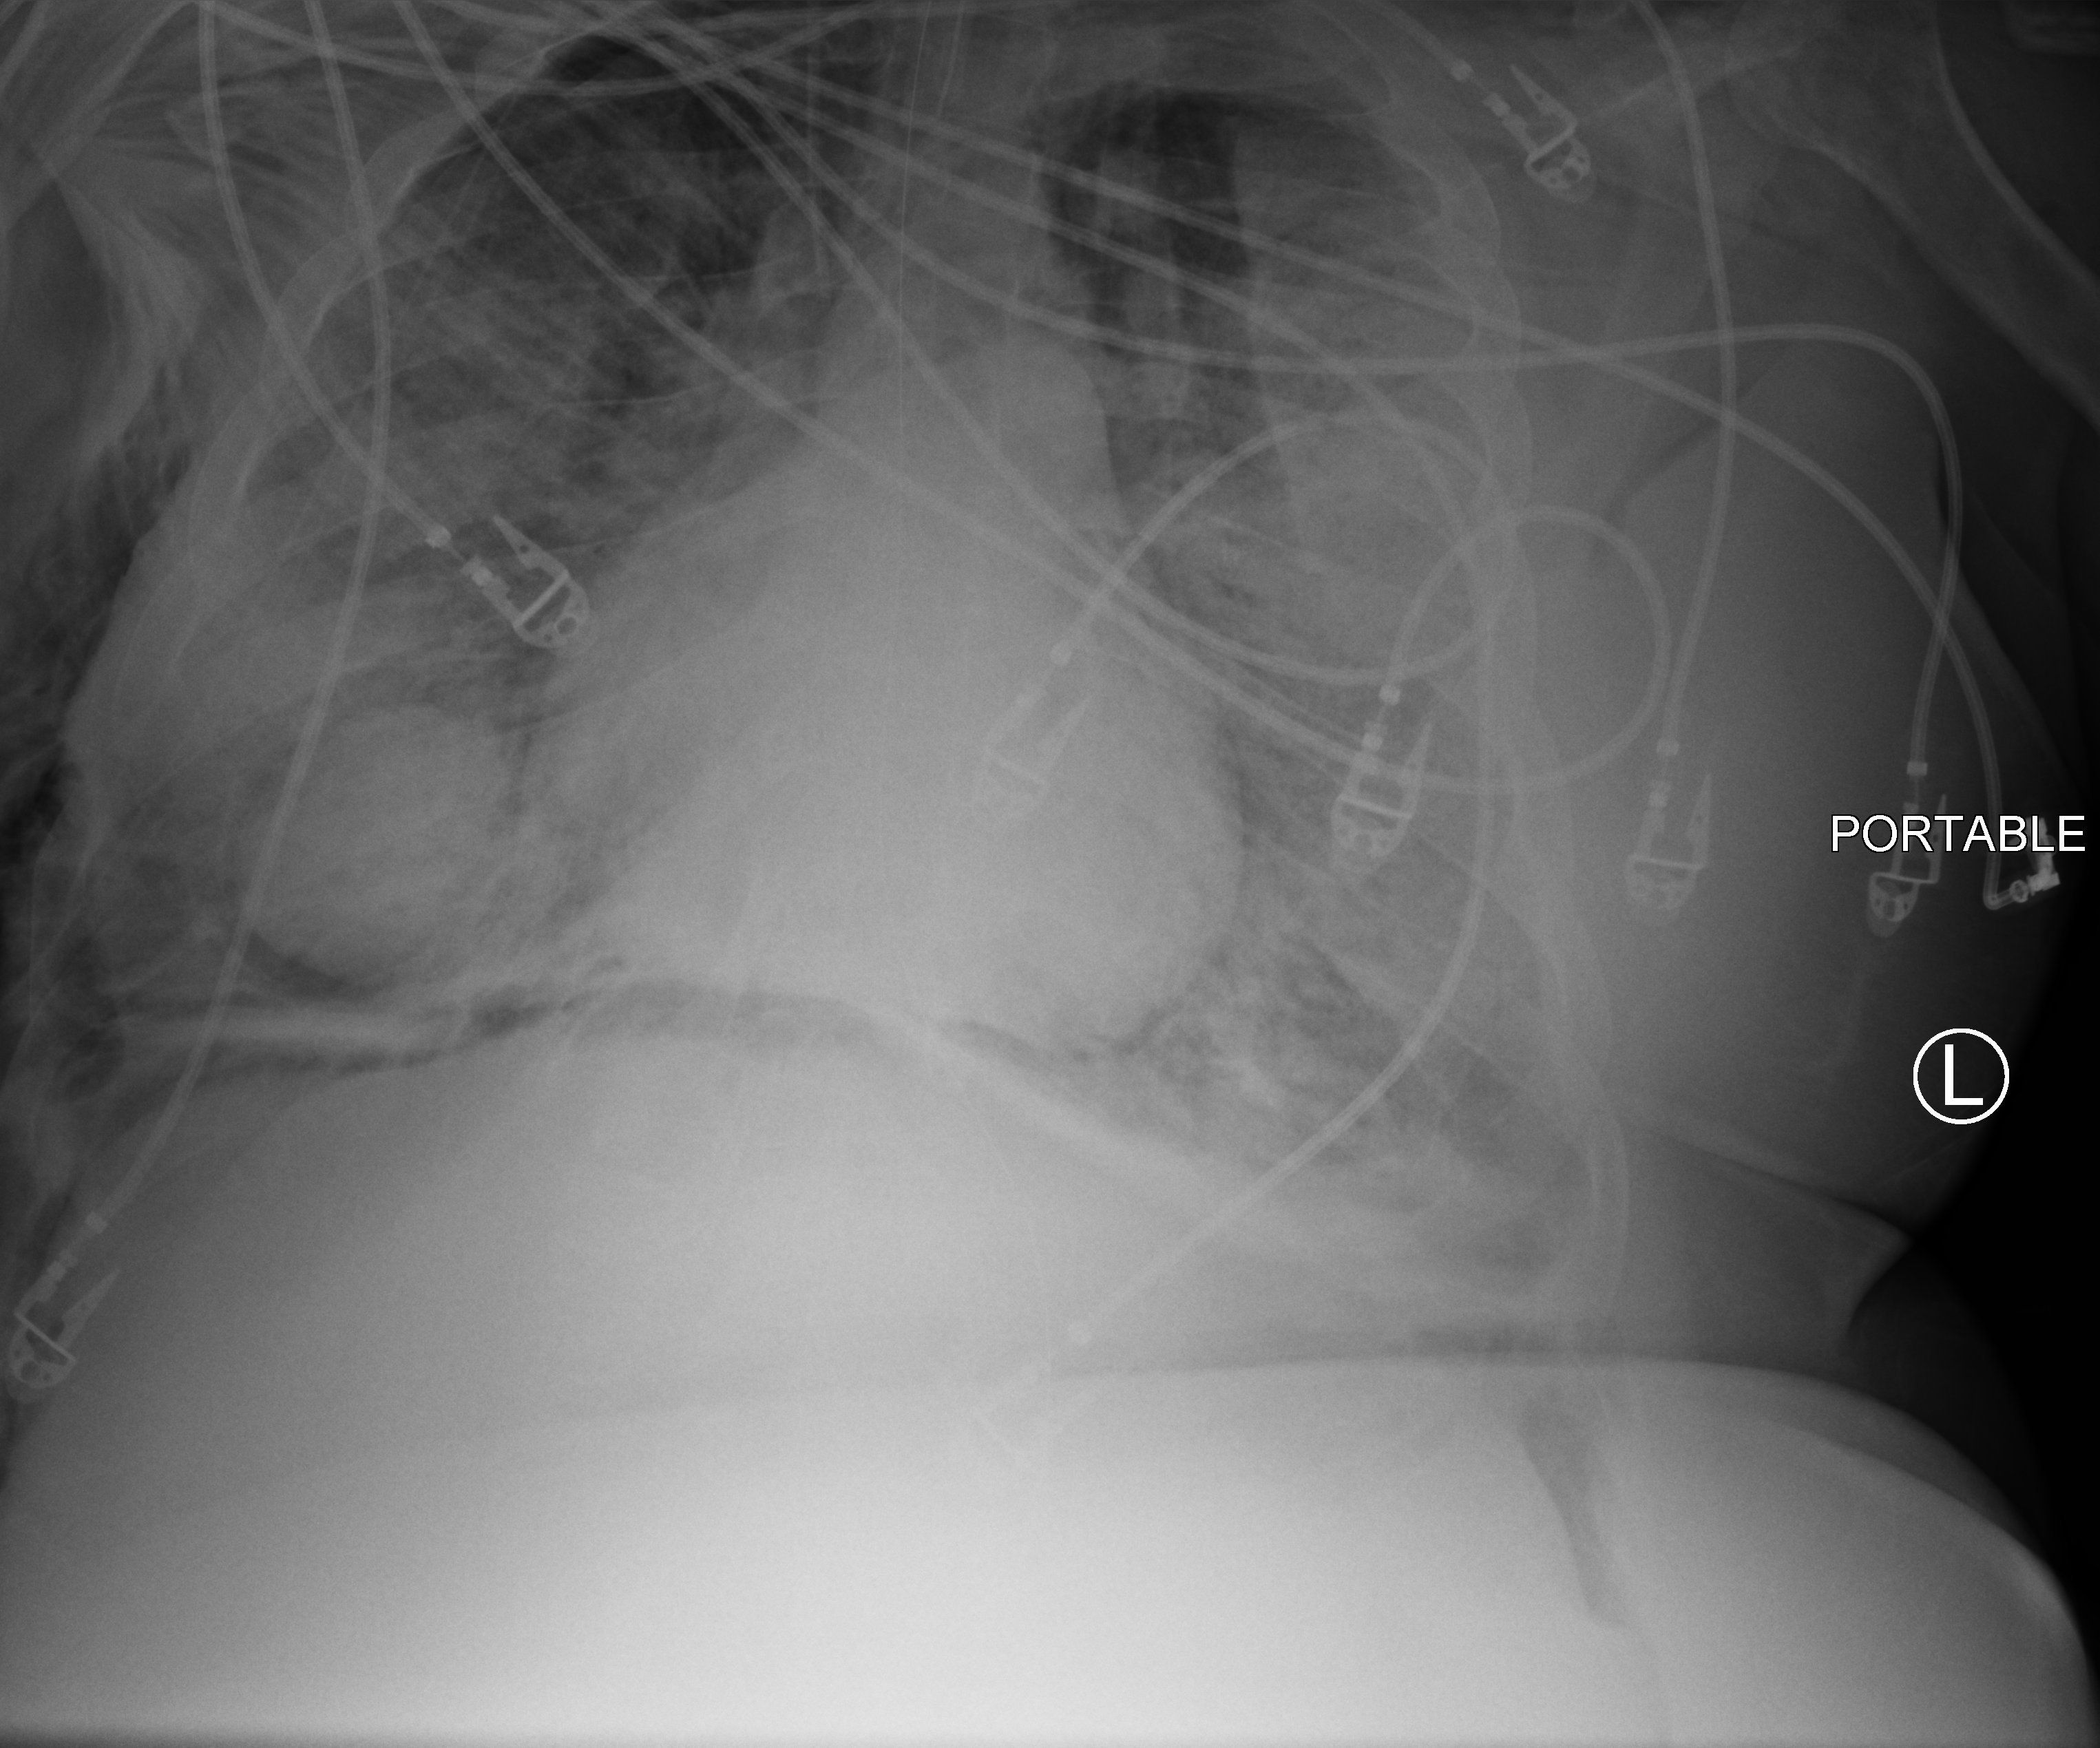
Portable chest radiograph. Patient hospitalised with COVID-19, aged 18–59 years.
From the hospital-stay record, not from the radiograph (when in the stay this image was taken is not recorded):
- mechanically ventilated during this hospital stay: yes
- hypertension (admission record): no